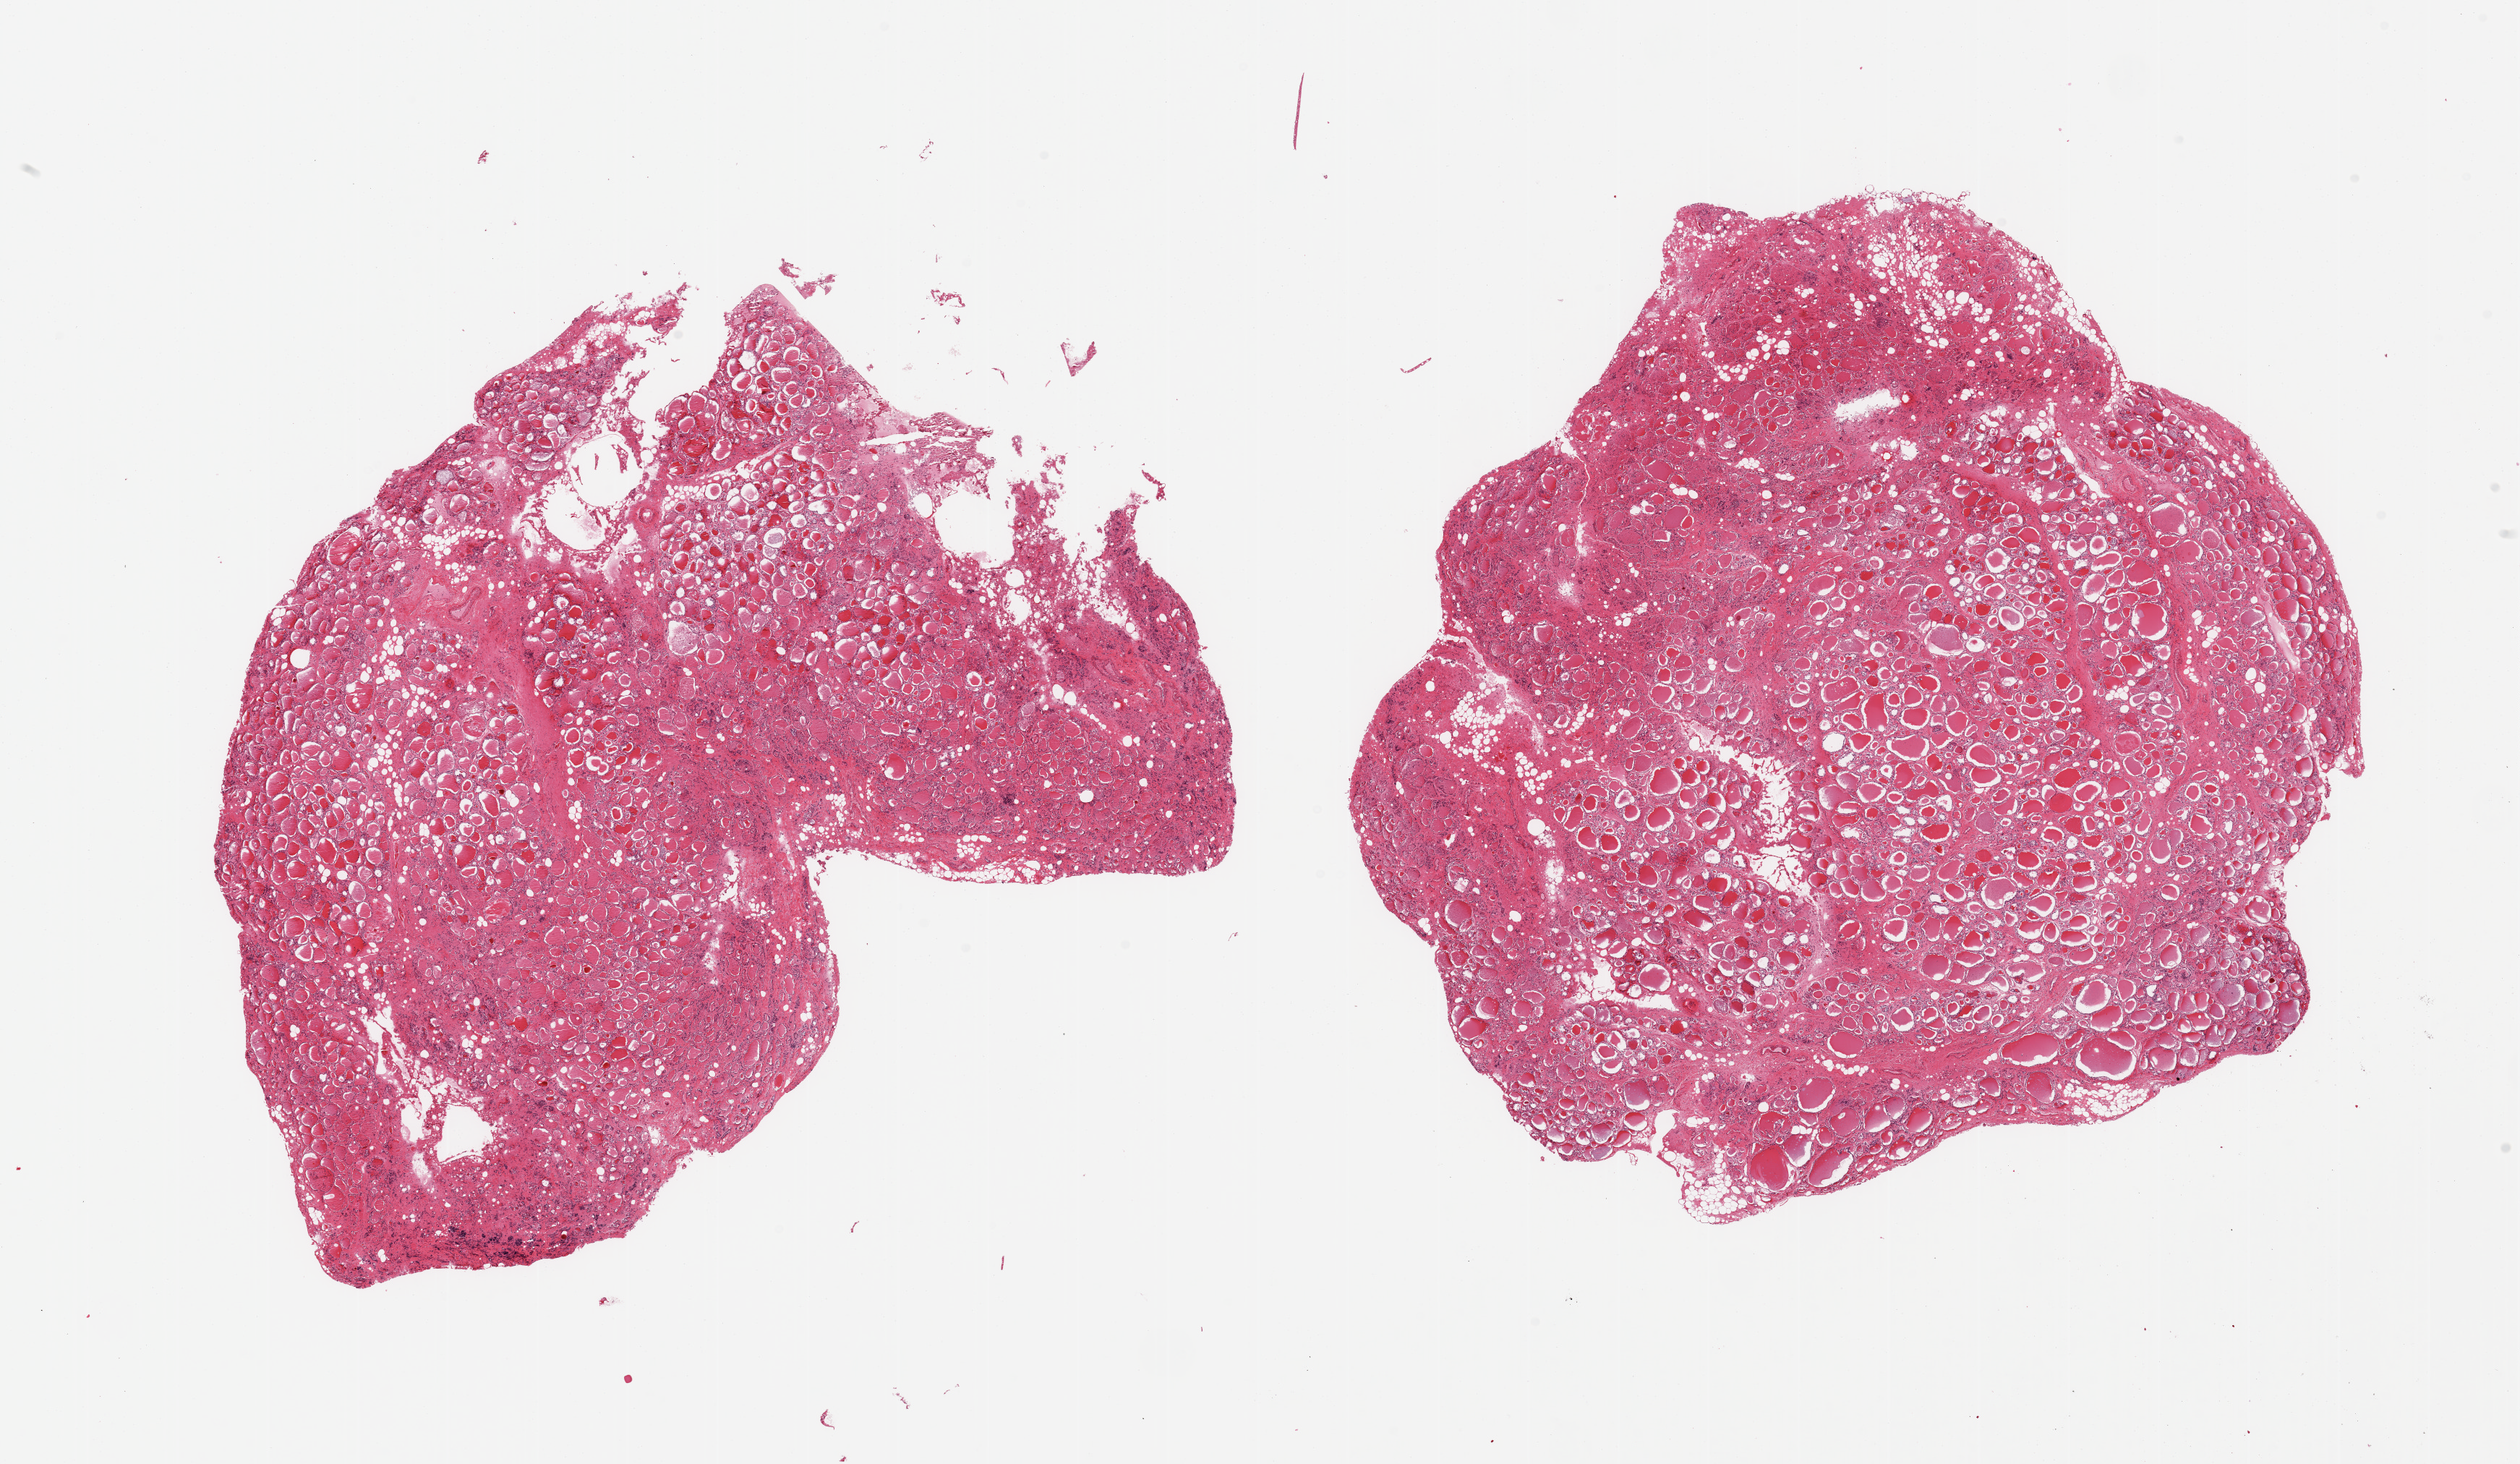
Haematoxylin and eosin whole-slide image, brightfield — shown as a low-resolution overview of the whole scanned area (about 27.6 x 16.0 mm); PAXgene-fixed paraffin-embedded (PFPE) section; section of thyroid (target tissue); donor tissue sample. Male donor.
Review note (as recorded): 2 pieces, moderately advanced autolysis.